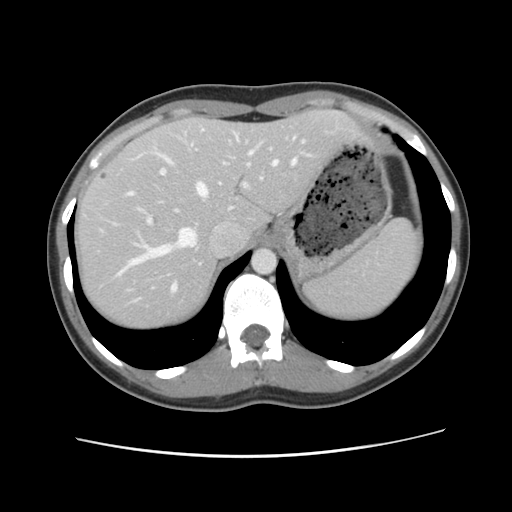
Contrast-enhanced abdominal CT, one axial slice; position 89 of 134 along the scan axis; intravenous contrast given; soft-tissue window (W 400 / L 40 HU); 2.5 mm slice thickness; 512 × 512 image matrix. Female patient, age 33 years. From the clinical record (not read from this slice): diagnosis: colorectal cancer liver metastases, imaged before liver resection; multiple liver metastases: yes; largest metastasis: 4.5 cm; disease in both lobes: yes.
Structures marked on this image (expert manual segmentation):
- hepatic veins: bounding box <119,133,304,292> (left, top, right, bottom; pixels)
- liver: <75,111,363,330>
- planned liver remnant (the part of the liver to remain after resection): <75,111,363,331>
- portal vein (with intrahepatic branches): <136,139,273,226>
- liver metastasis: <99,172,109,181>